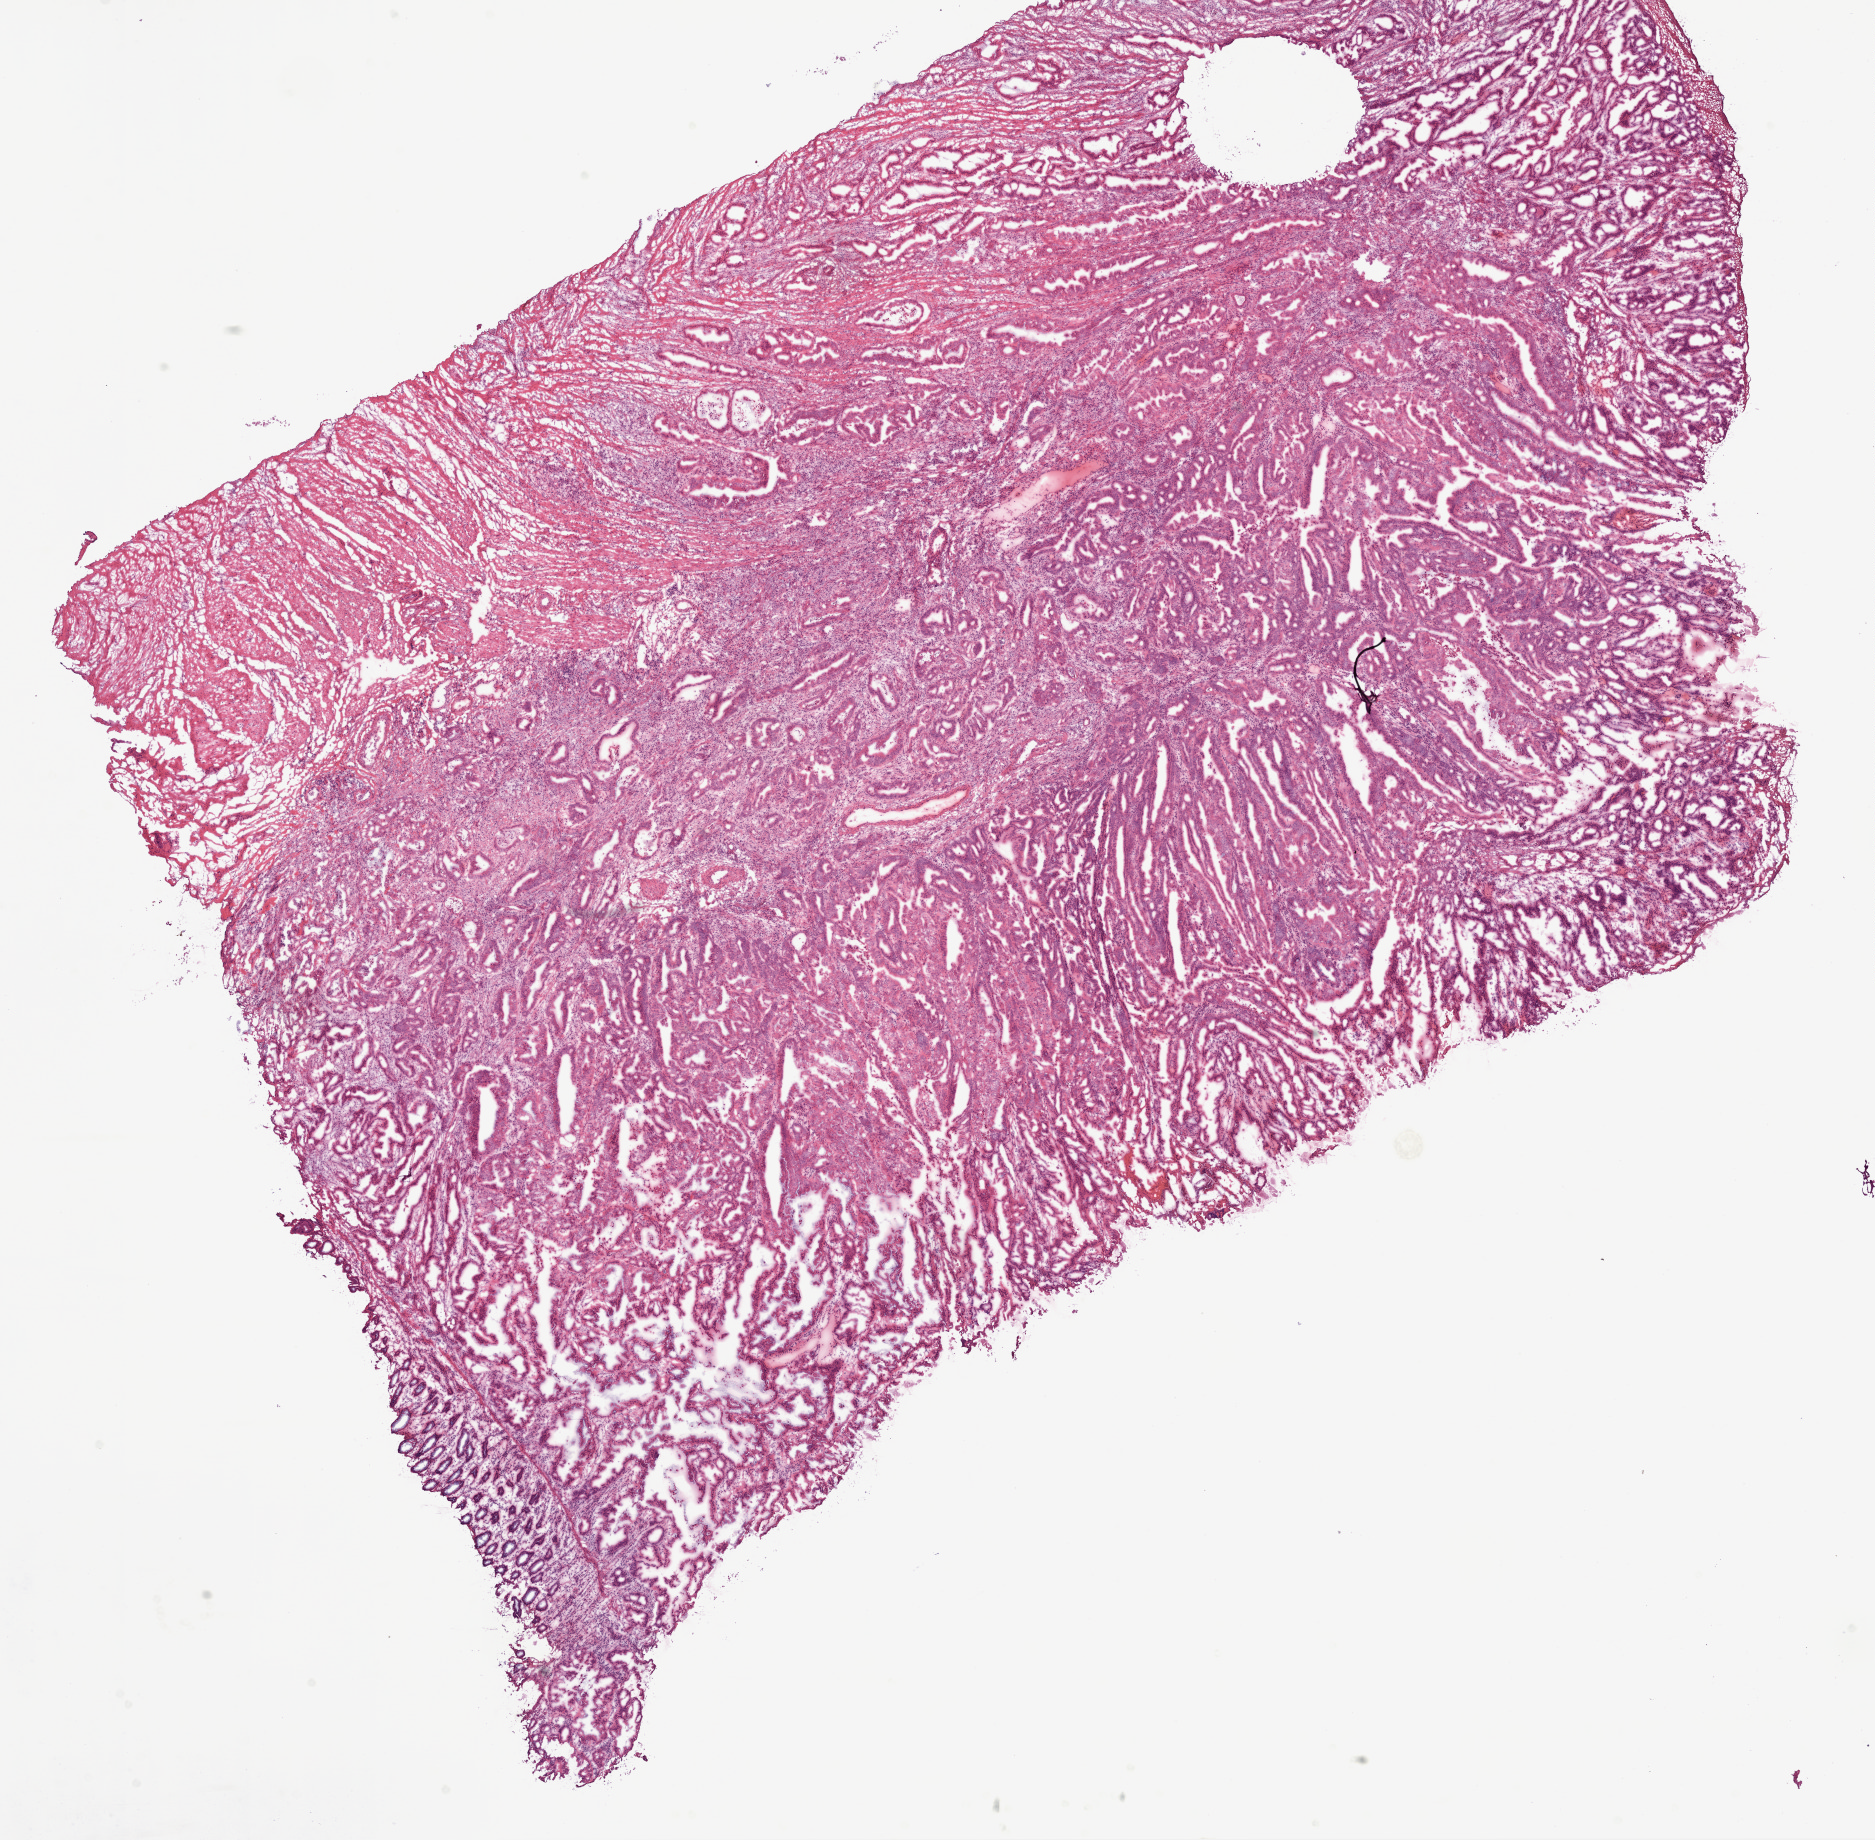
H&E whole-slide image — whole scanned area (about 15.0 x 14.8 mm) shown as a low-resolution overview. Frozen section from the top of the tissue portion. Sample: primary tumour, colon. Patient: male, age at initial diagnosis 45 years. Composition of this section per pathologist review: tumour cells 40%, tumour nuclei 60%, normal cells 0%, stromal cells 60%, necrosis 0%.
Pathologic diagnosis: Adenocarcinoma, NOS. TNM: T3 N0 M0. AJCC pathologic stage: IIA (6th edition).